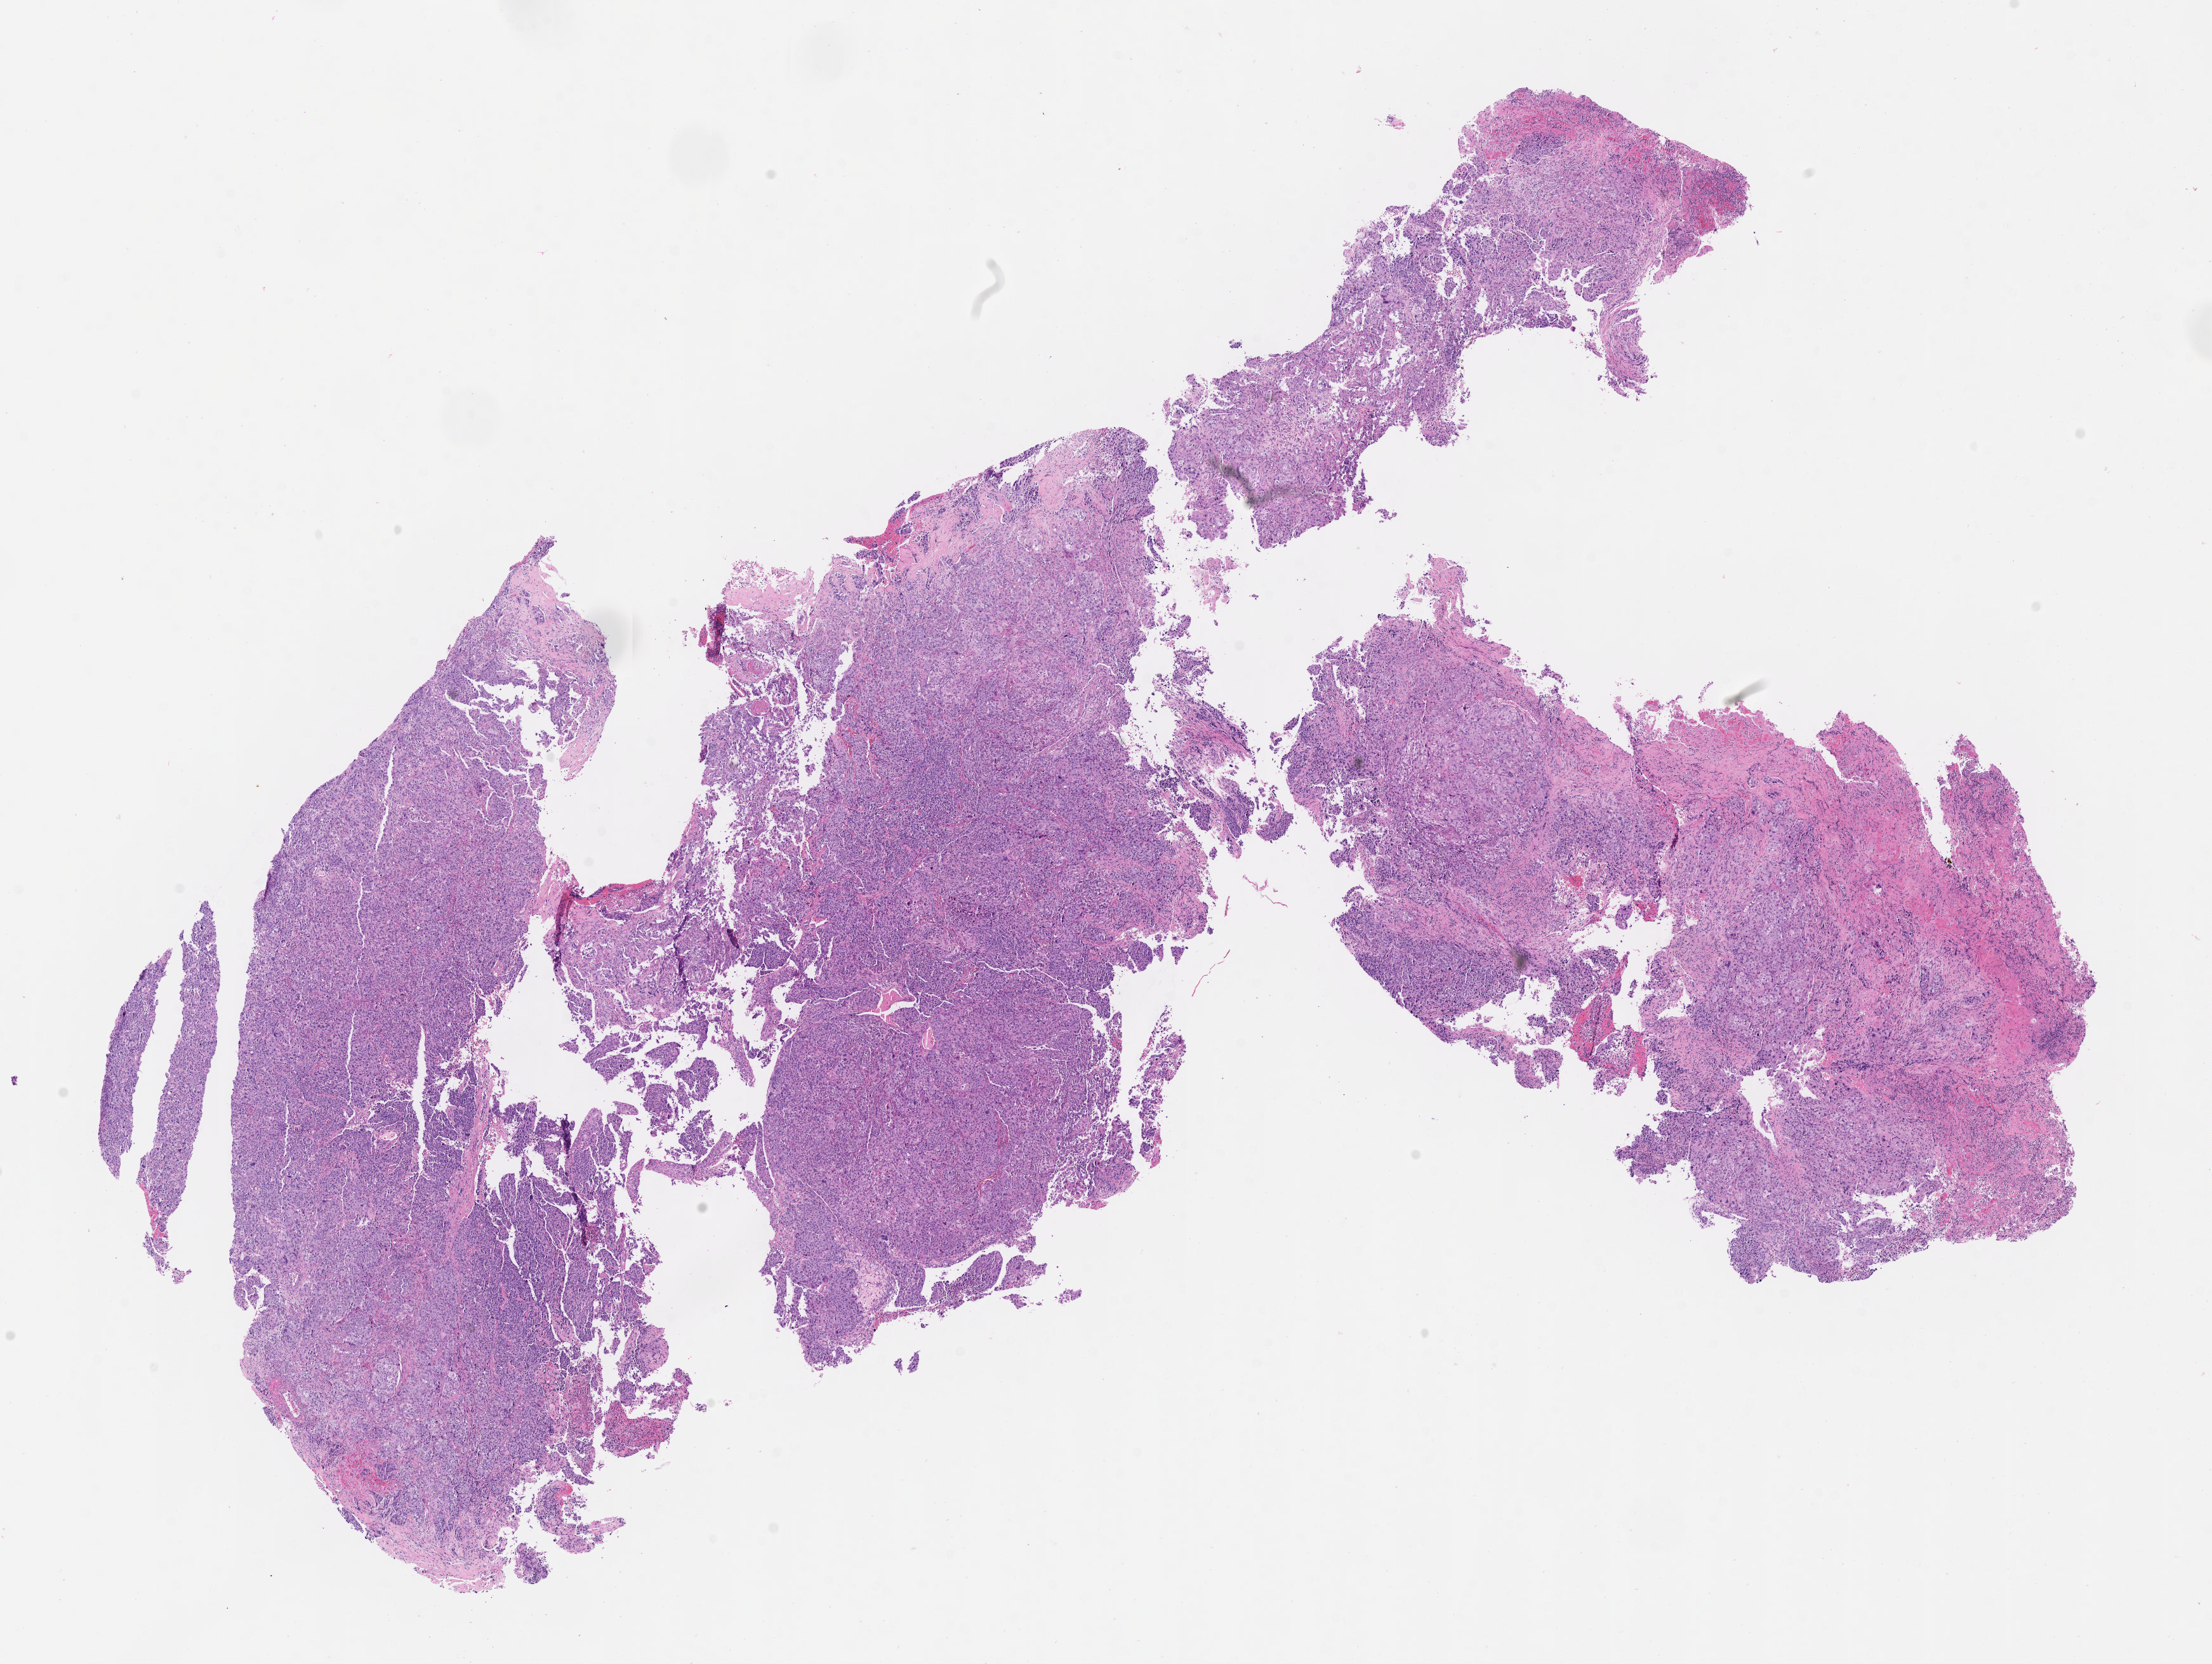
Whole-slide image, hematoxylin and eosin (H&E) stain, shown as a low-resolution overview of the whole scanned area (about 14.1 x 10.6 mm). Specimen: tumor tissue. Anatomic site: cervix. Patient female; age 54 years.
Histologic diagnosis: Adenocarcinoma, NOS.